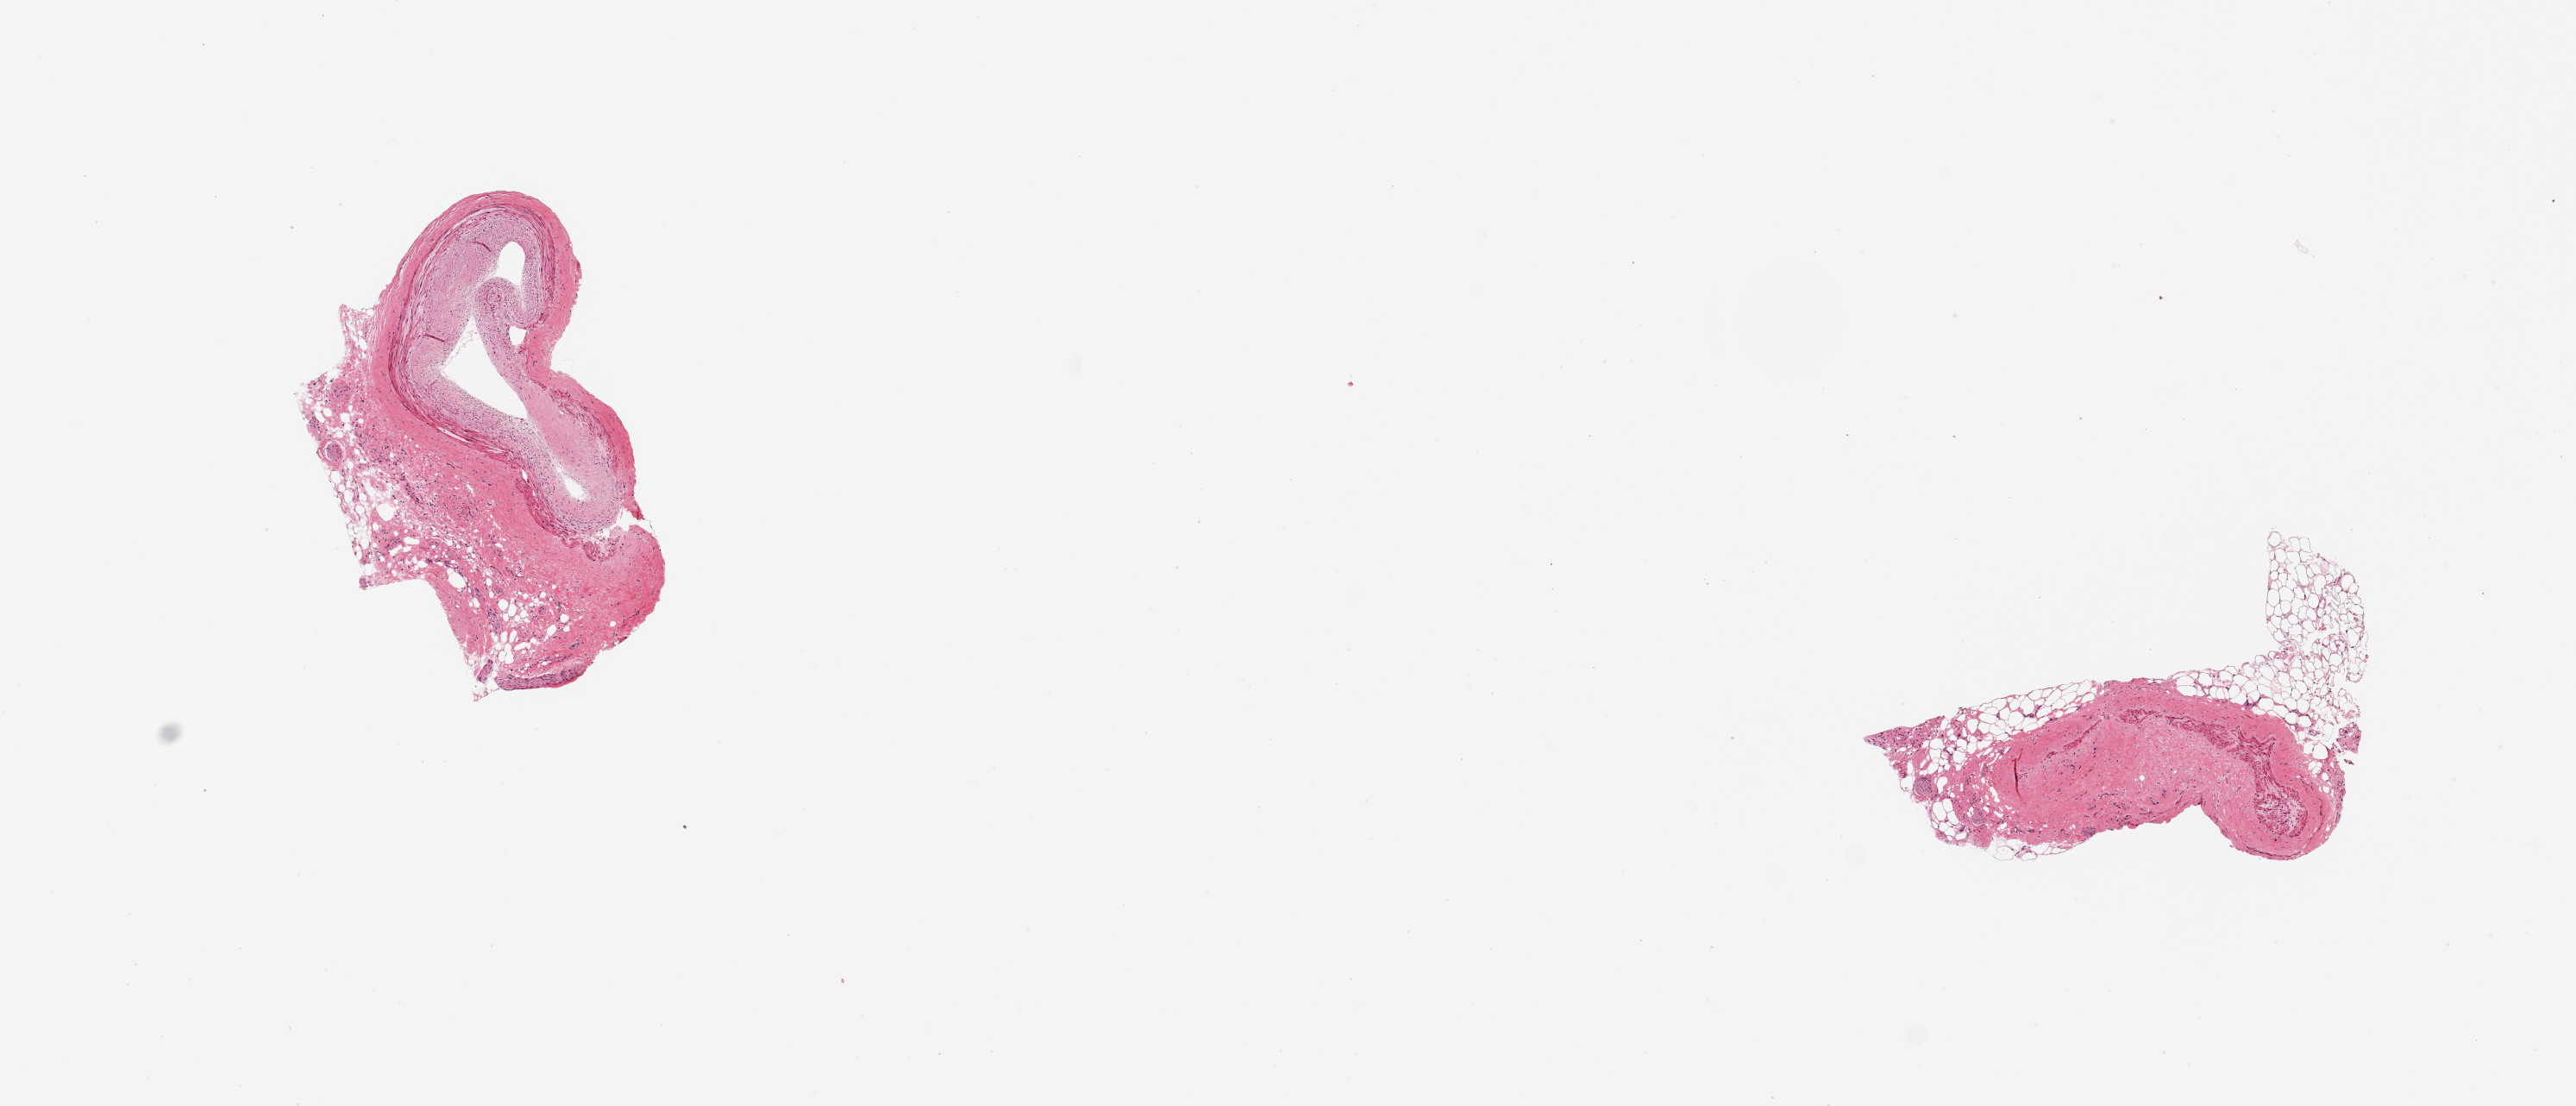
Digitized hematoxylin and eosin (H&E)-stained section — whole scanned area (about 11.8 x 5.1 mm, slide scanned at 20x) shown as a low-resolution overview. PAXgene-fixed, paraffin-embedded tissue. Section of coronary artery (target tissue). Donor tissue sample.
• pathologist's review note for this sample: 2 pieces; atherosclerotic plaque and attached adventitia with external fat merasuring up to 0.8mm